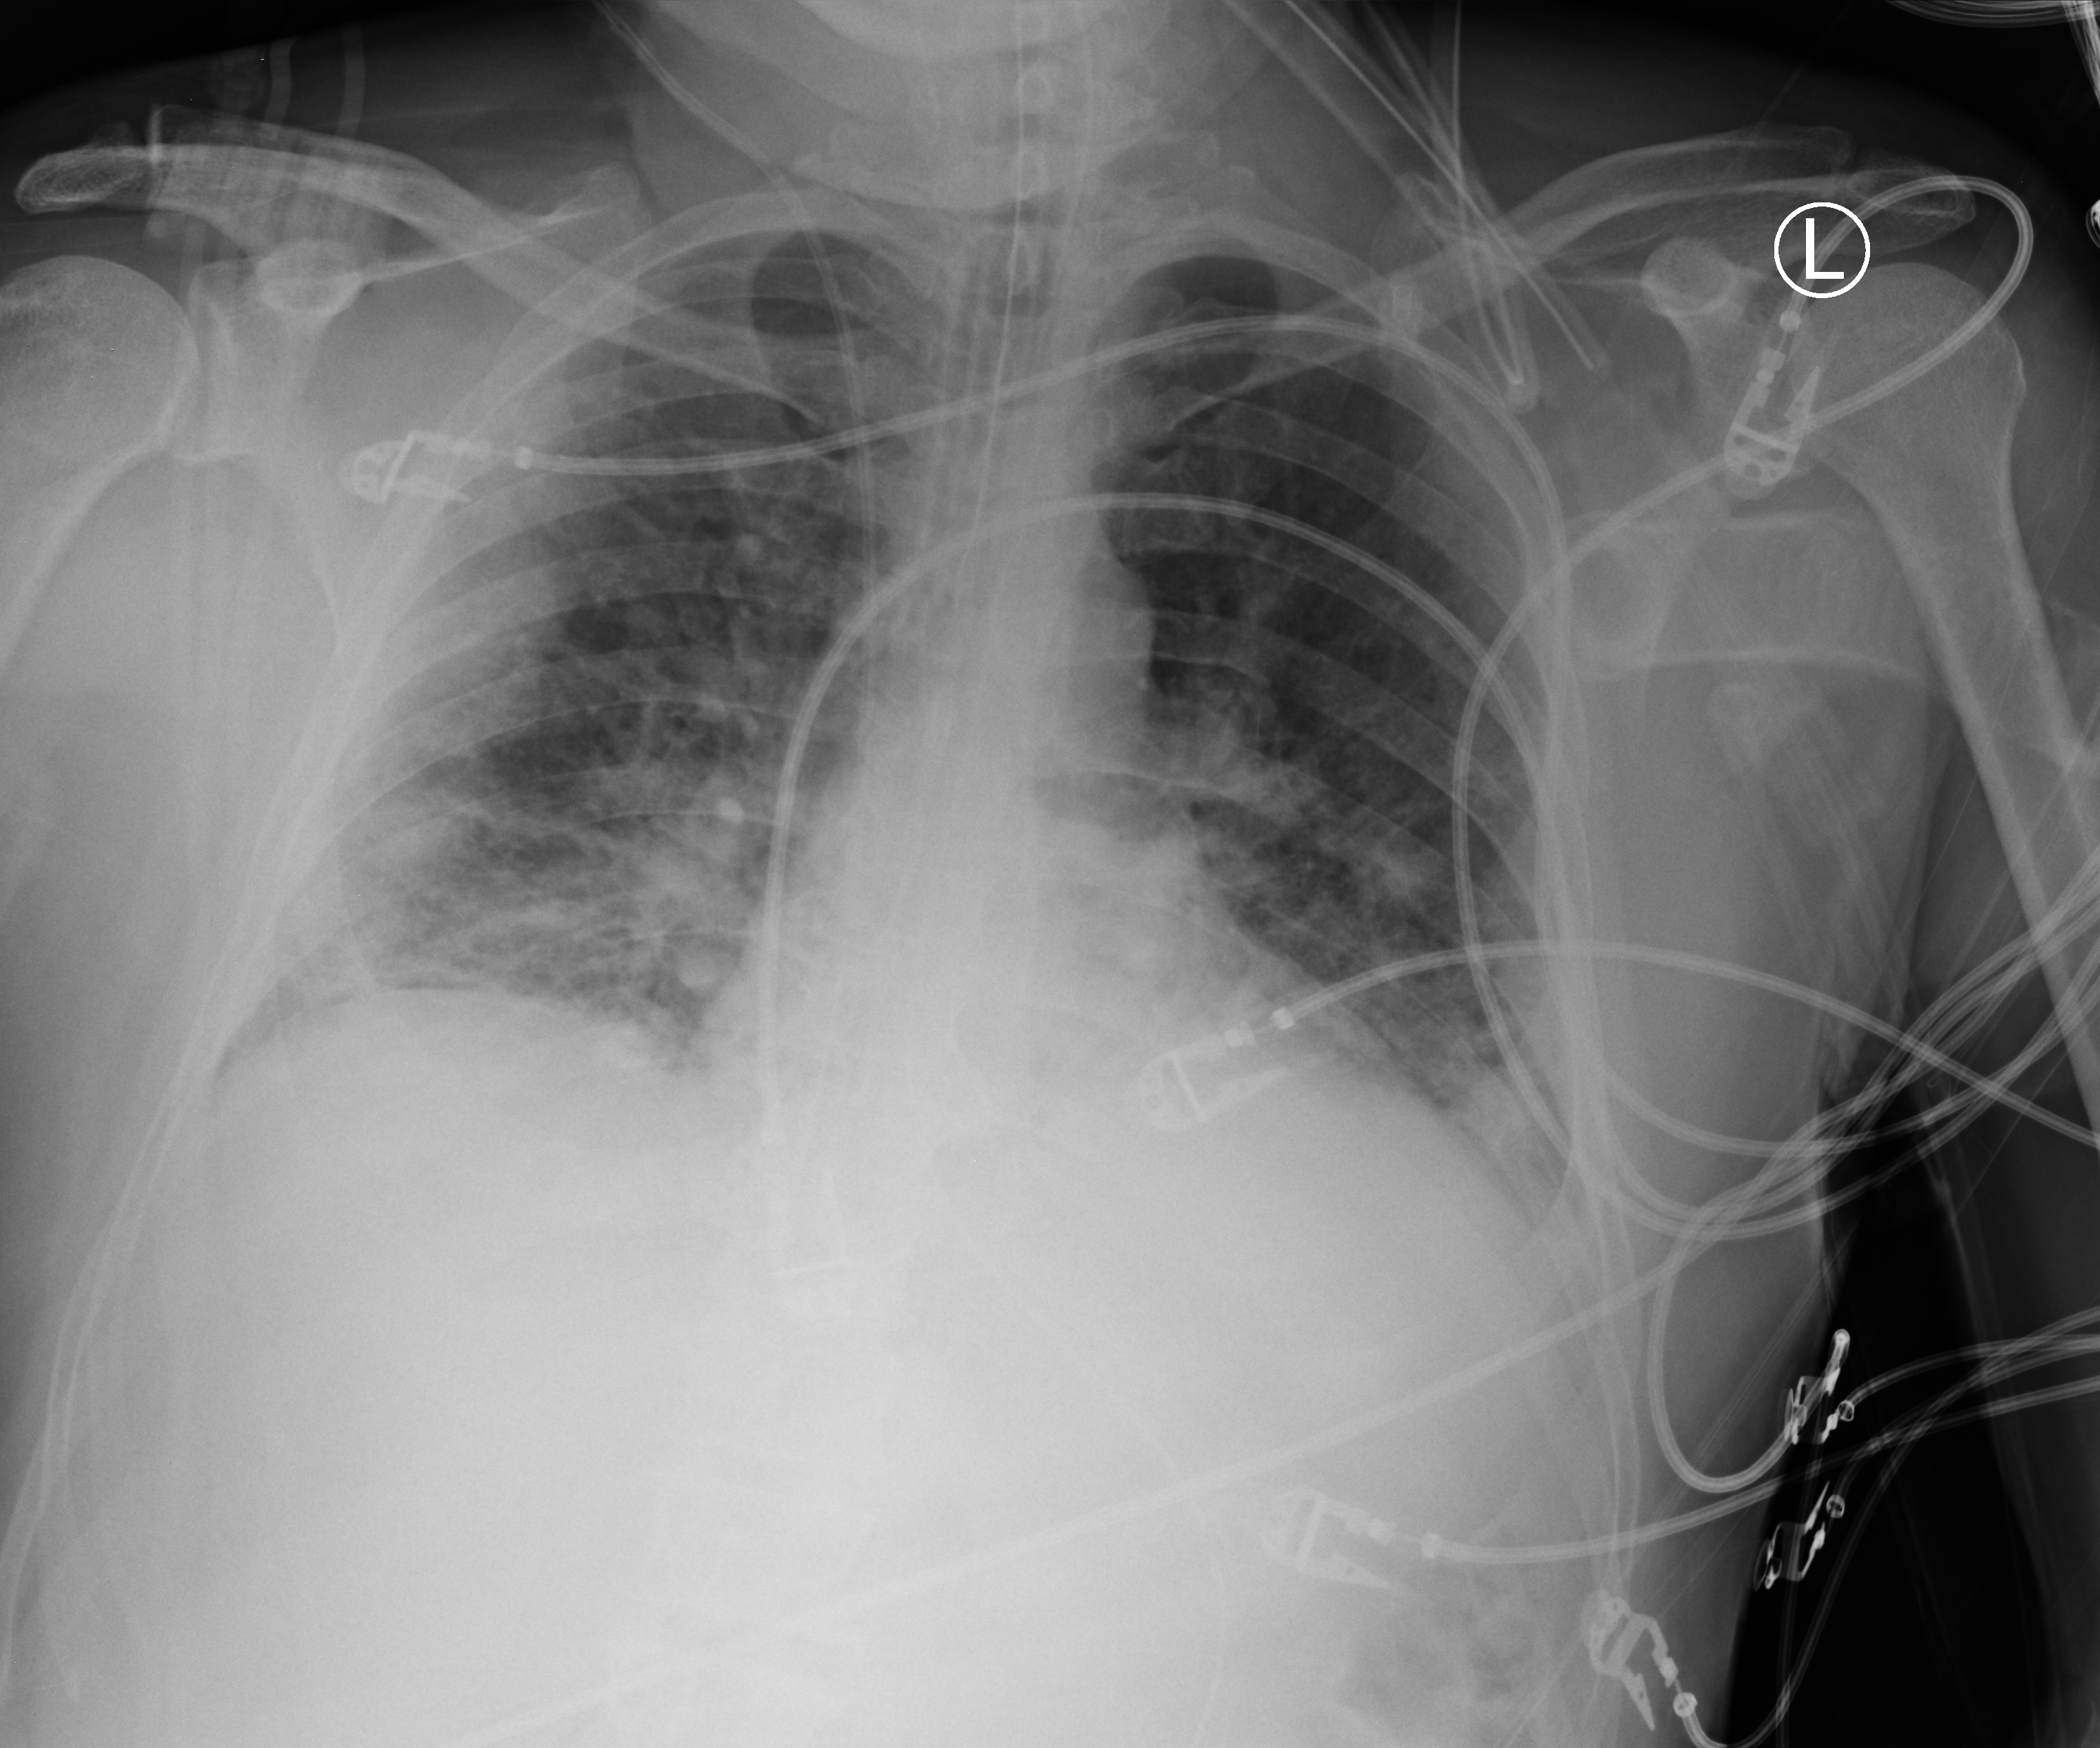
Portable chest radiograph, anteroposterior (AP) projection. Patient hospitalised with COVID-19; male, aged 18–59 years.
Hospital-stay facts (about this admission, not read from this image; timing relative to this image not recorded):
- mechanically ventilated during this hospital stay: yes
- admitted to intensive care during this hospital stay: yes